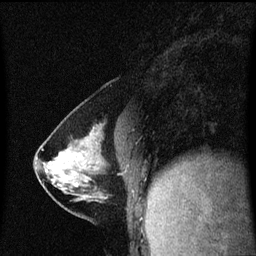
Breast MRI (dynamic contrast-enhanced), one sagittal slice; position 24 of 60 along the scan axis; dynamic contrast-enhanced series, image 2 of 3 at this slice position (ordered by acquisition); 1.5 T; TE 4.2 ms, TR 8.4 ms; 2 mm slice thickness; 256 × 256 image matrix, field of view 200 × 200 mm. Patient: female, 40 years. From the clinical record (not read from this slice): setting: breast cancer imaged before/during neoadjuvant chemotherapy; receptor status: triple-negative.
Structures marked on this image (semi-automatic segmentation, software-assisted and operator-edited):
- analysis volume of interest (the breast-tissue region the enhancement analysis was run in; not a lesion): bounding box [x1, y1, x2, y2] px = [34, 142, 108, 199]
- tumour enhancement mask (voxels above the 70 % enhancement threshold inside the analysis volume of interest): [55, 158, 62, 163]